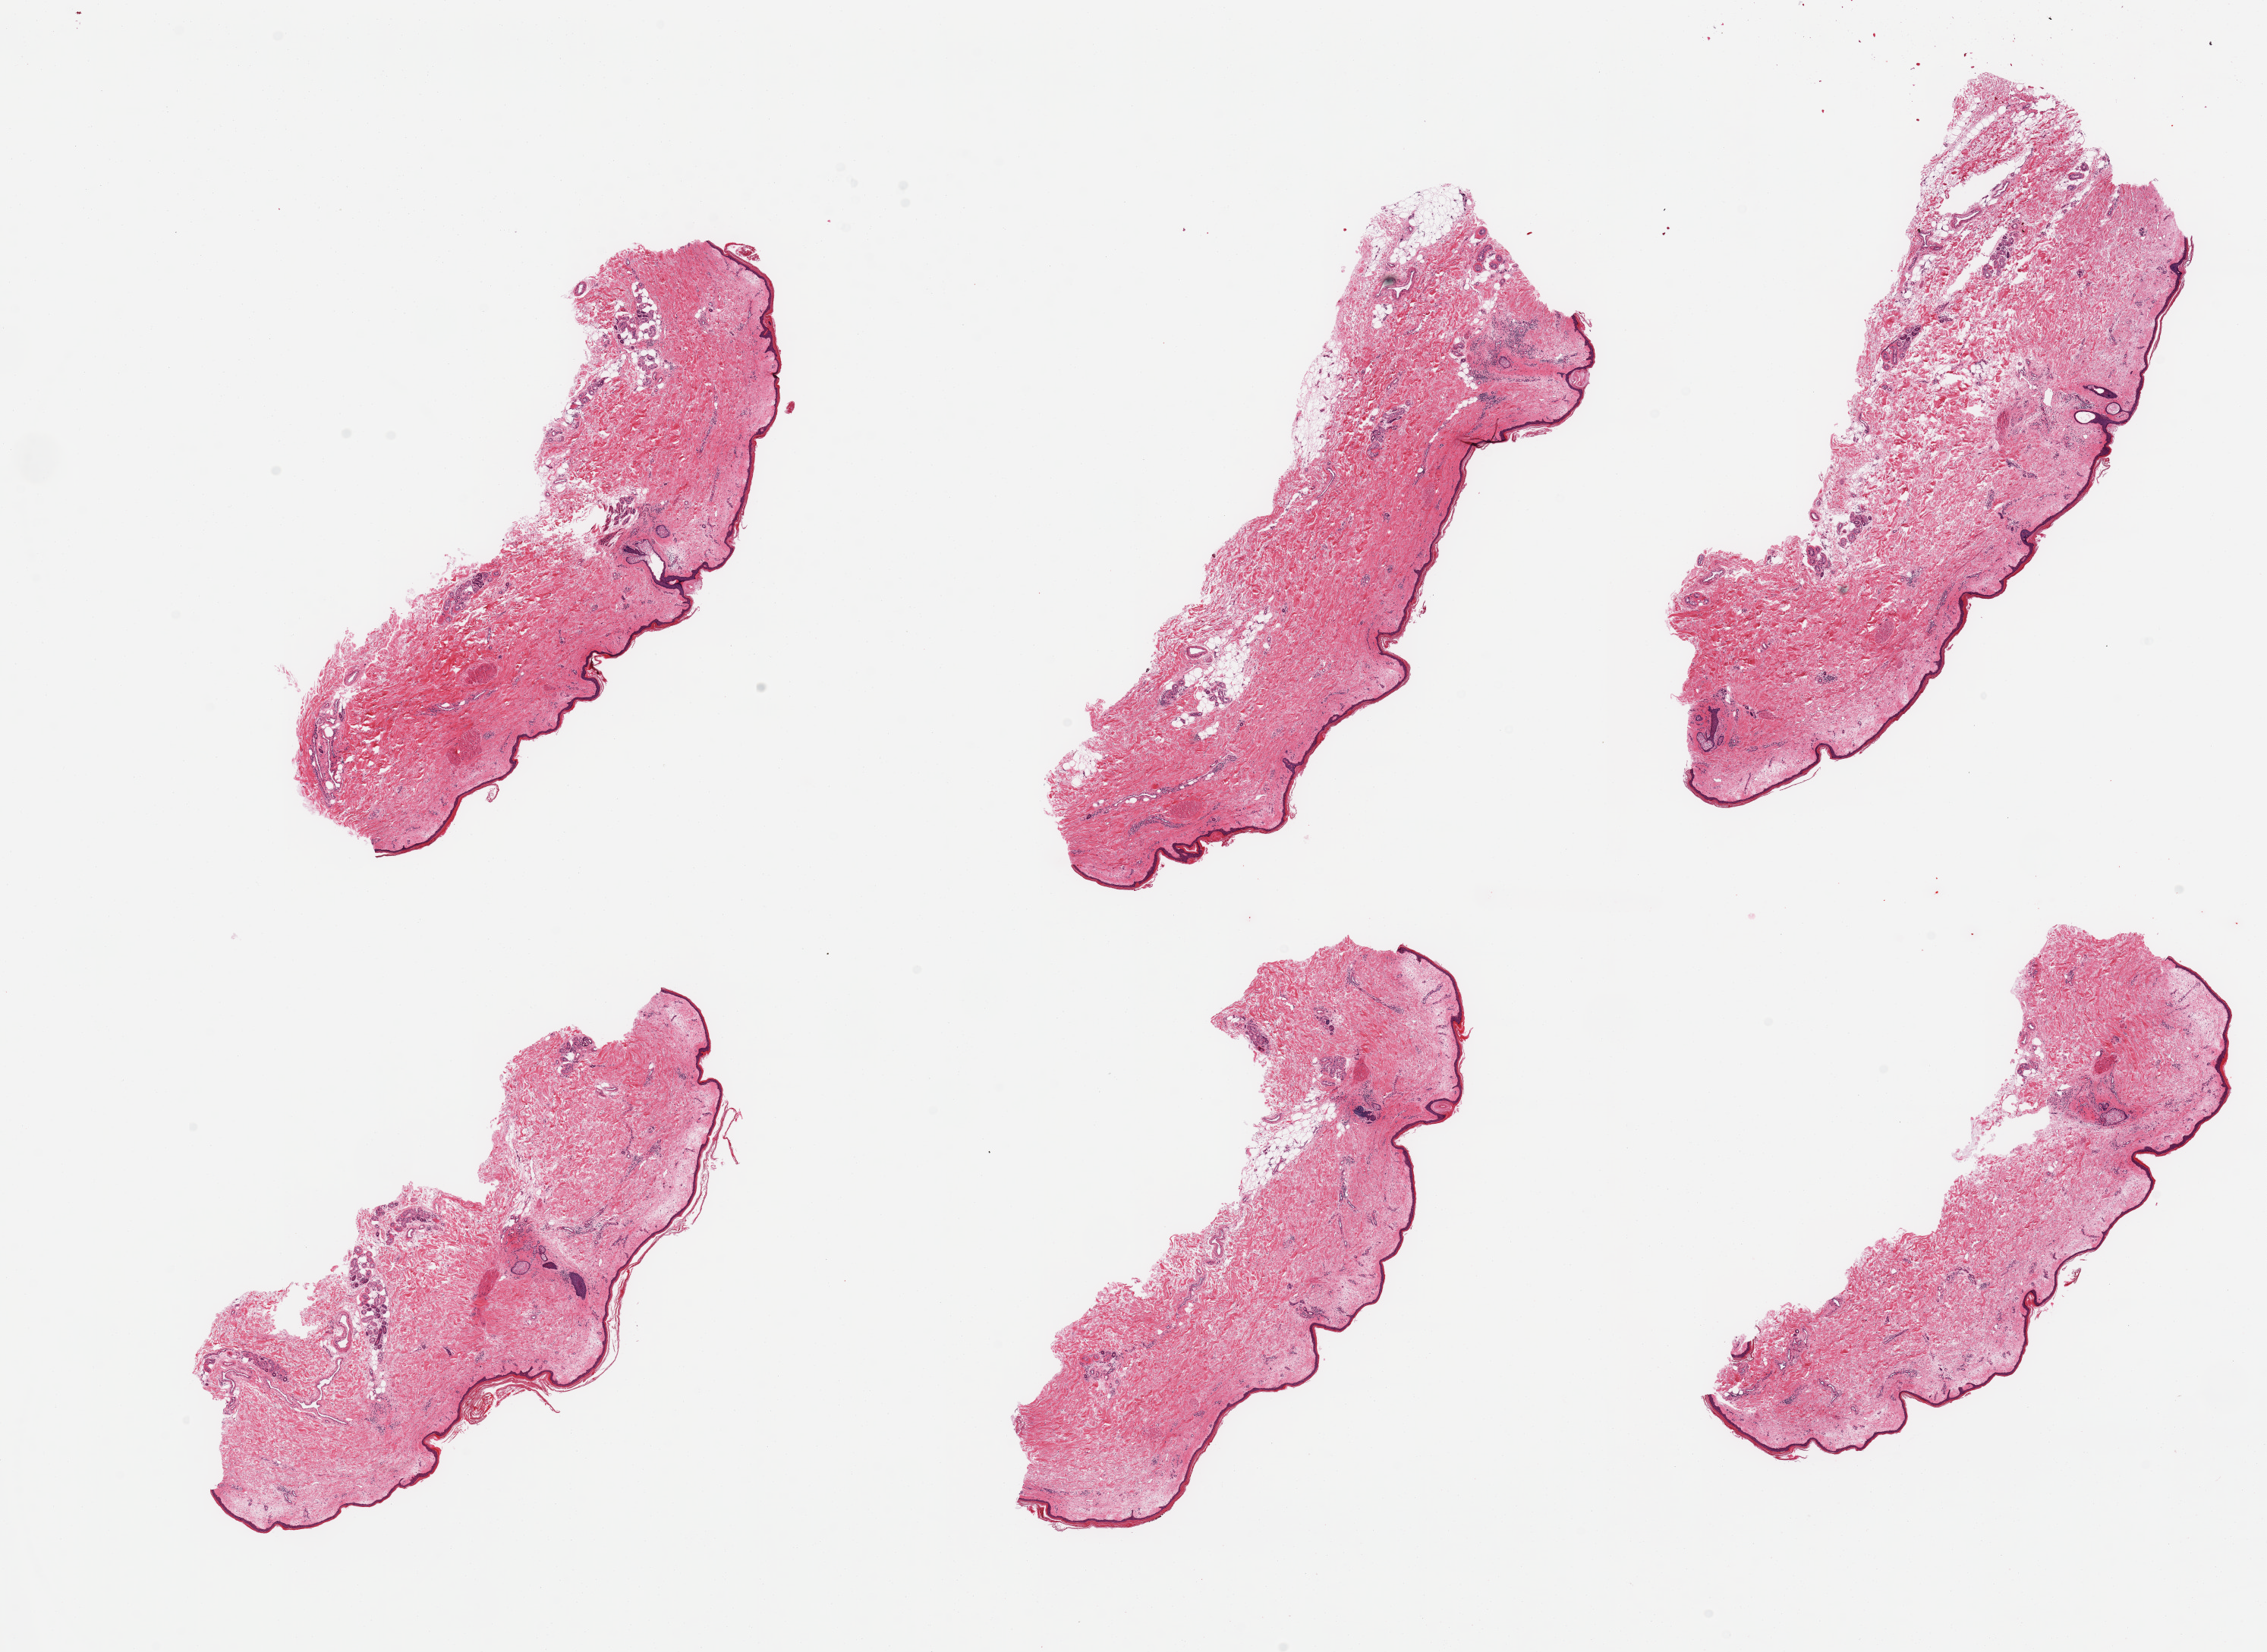
Whole-slide image, H&E stain — shown as a low-resolution overview of the whole scanned area (about 23.6 x 17.2 mm). PAXgene-fixed paraffin-embedded (PFPE) section. Target tissue: skin of lower leg. Tissue donor sample.
Pathologist's review note for this sample: 6 pieces; 5% dermal fat; well trimmed.